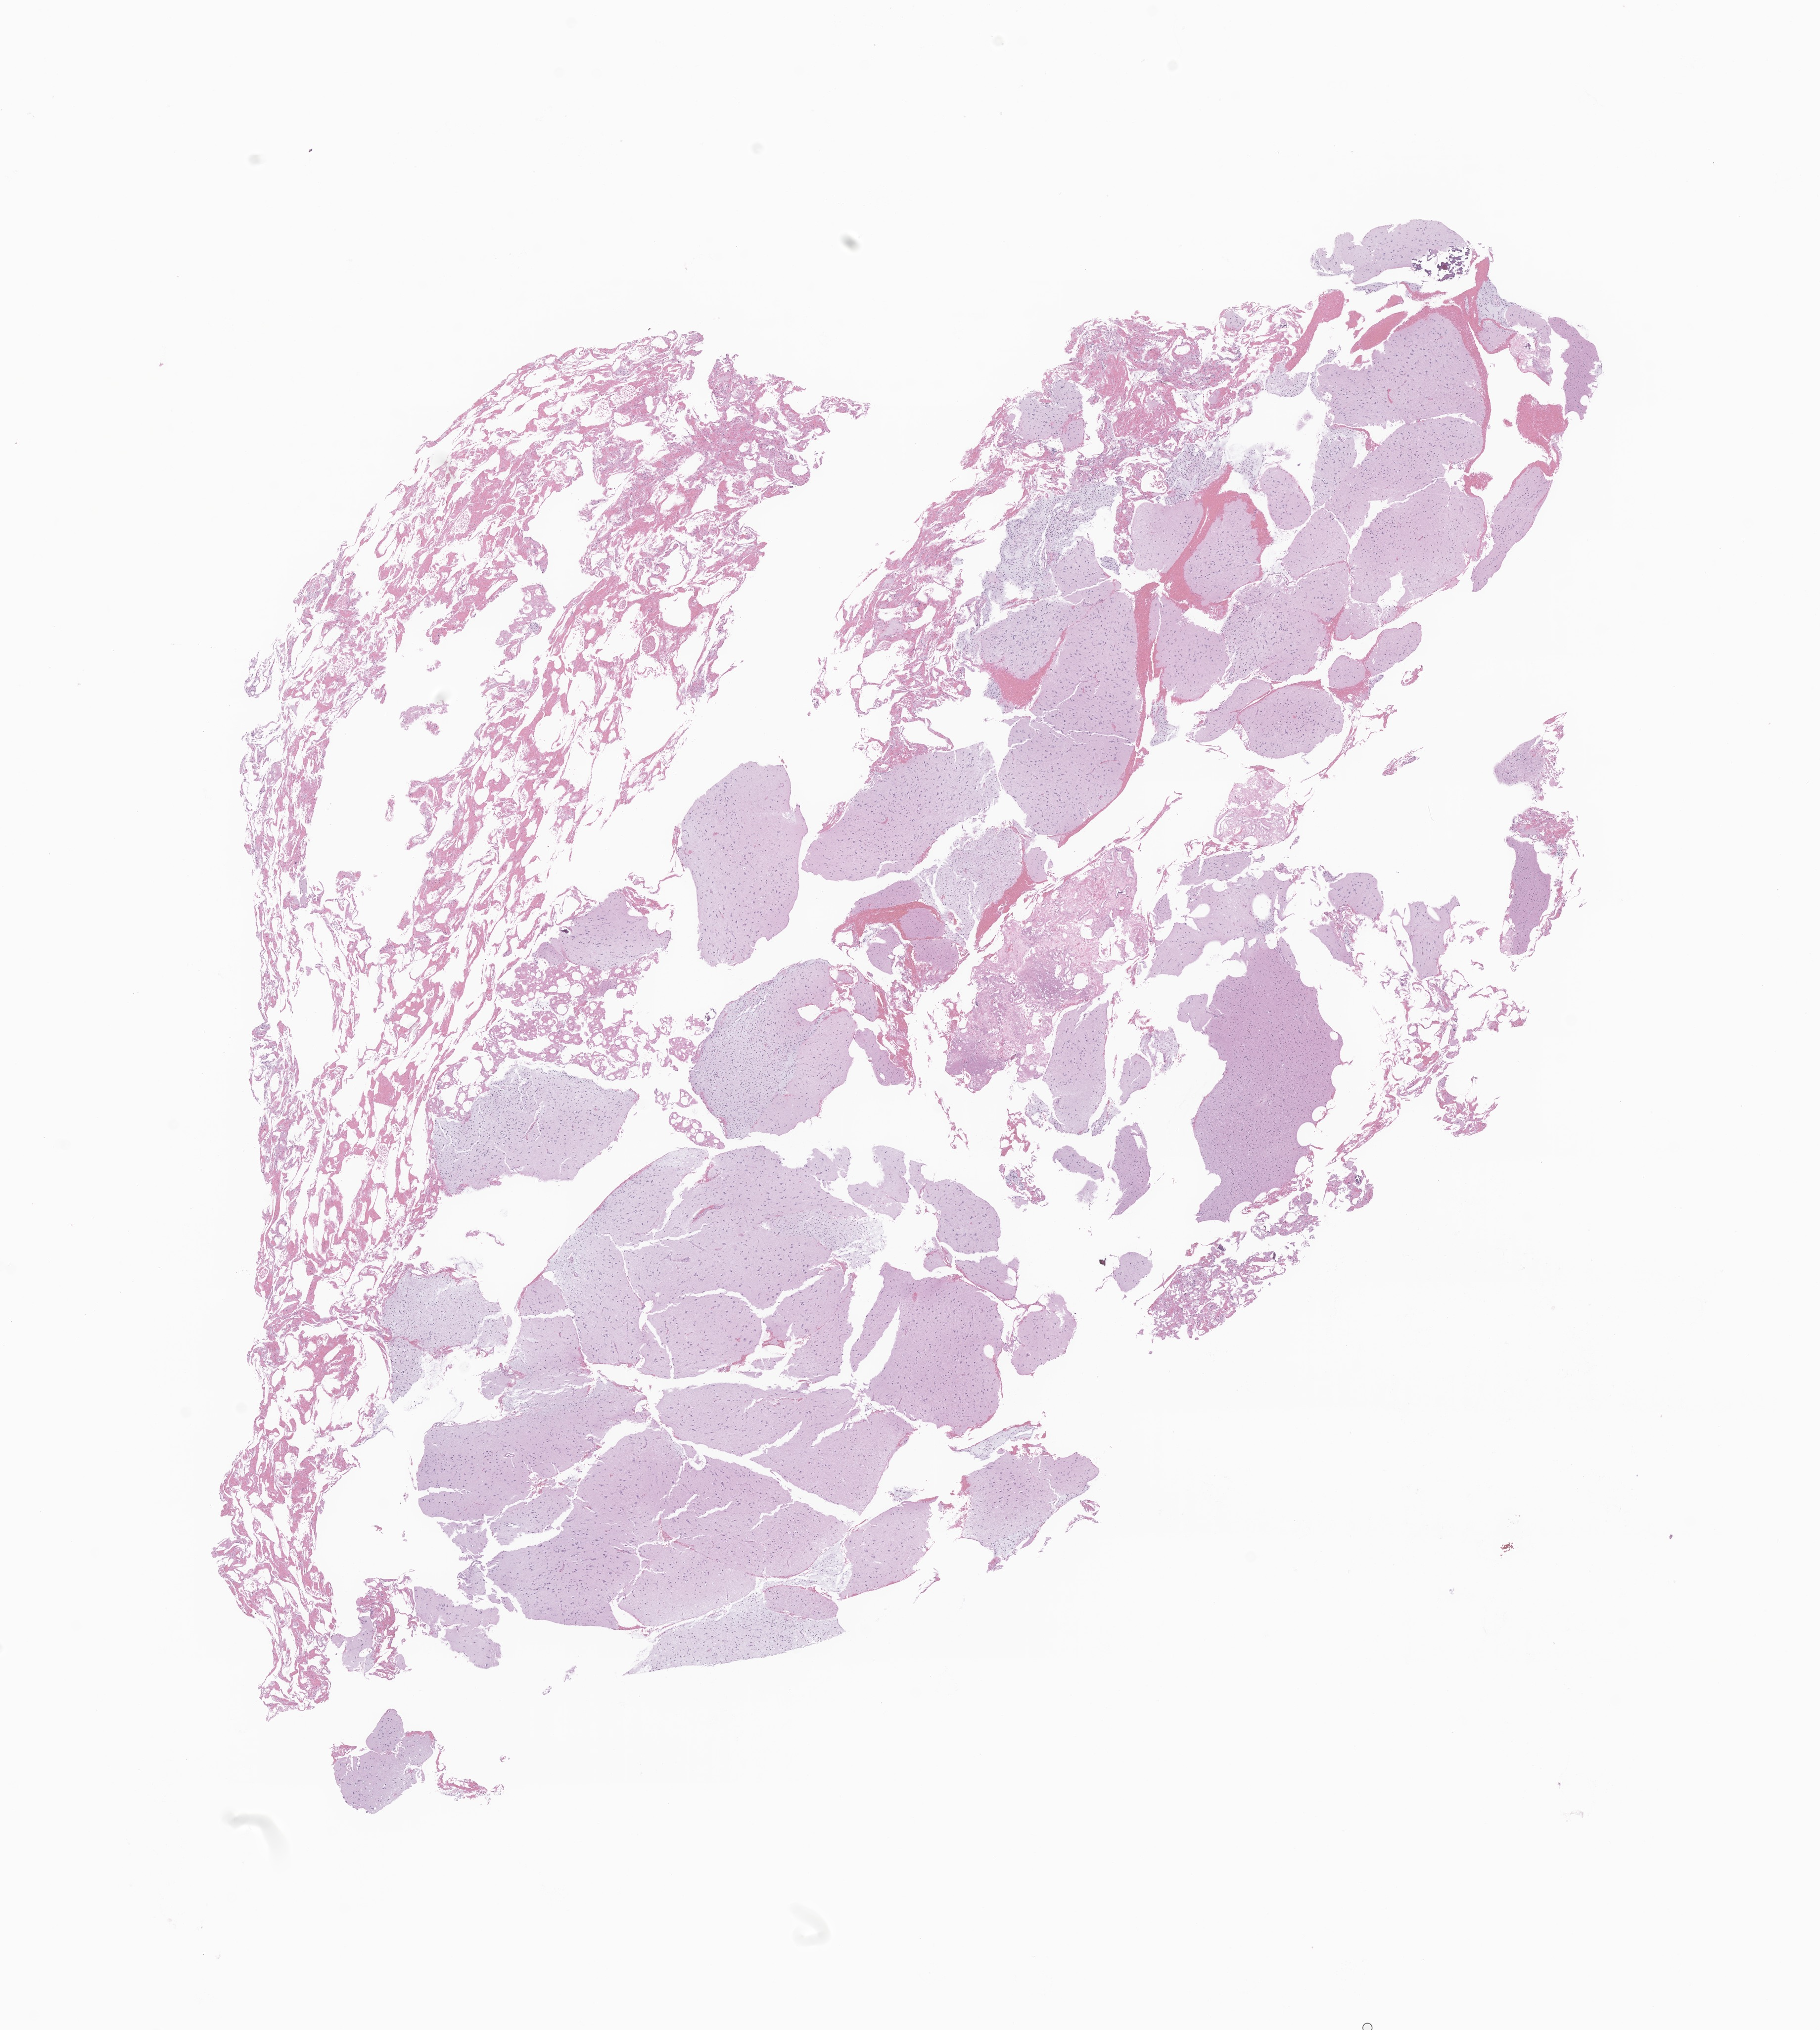
H&E whole-slide image of tumor tissue from the frontal lobe — whole scanned area (about 15.5 x 17.3 mm) shown as a low-resolution overview. Formalin-fixed paraffin-embedded section. Patient: male, age 138 months (11 years 6 months).
Recorded diagnosis: Dysembryoplastic neuroepithelial tumor.